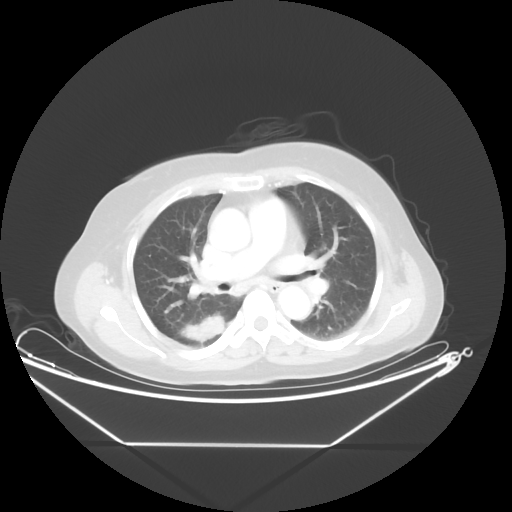
Chest CT, one axial slice. Position 27 of 48 along the scan axis. Reconstruction kernel STANDARD. 100 kVp. Lung window (W 1500 / L -600 HU). 5 mm slice thickness. 512 × 512 image matrix. Patient: female, 62 years. From the clinical record (not read from this slice): clinical TNM (as recorded): T1c N0 M0.
Annotated regions visible in this slice (bounding box drawn by a radiologist):
- lung tumour (recorded histology: adenocarcinoma): box from (x=180, y=310) to (x=237, y=361) px